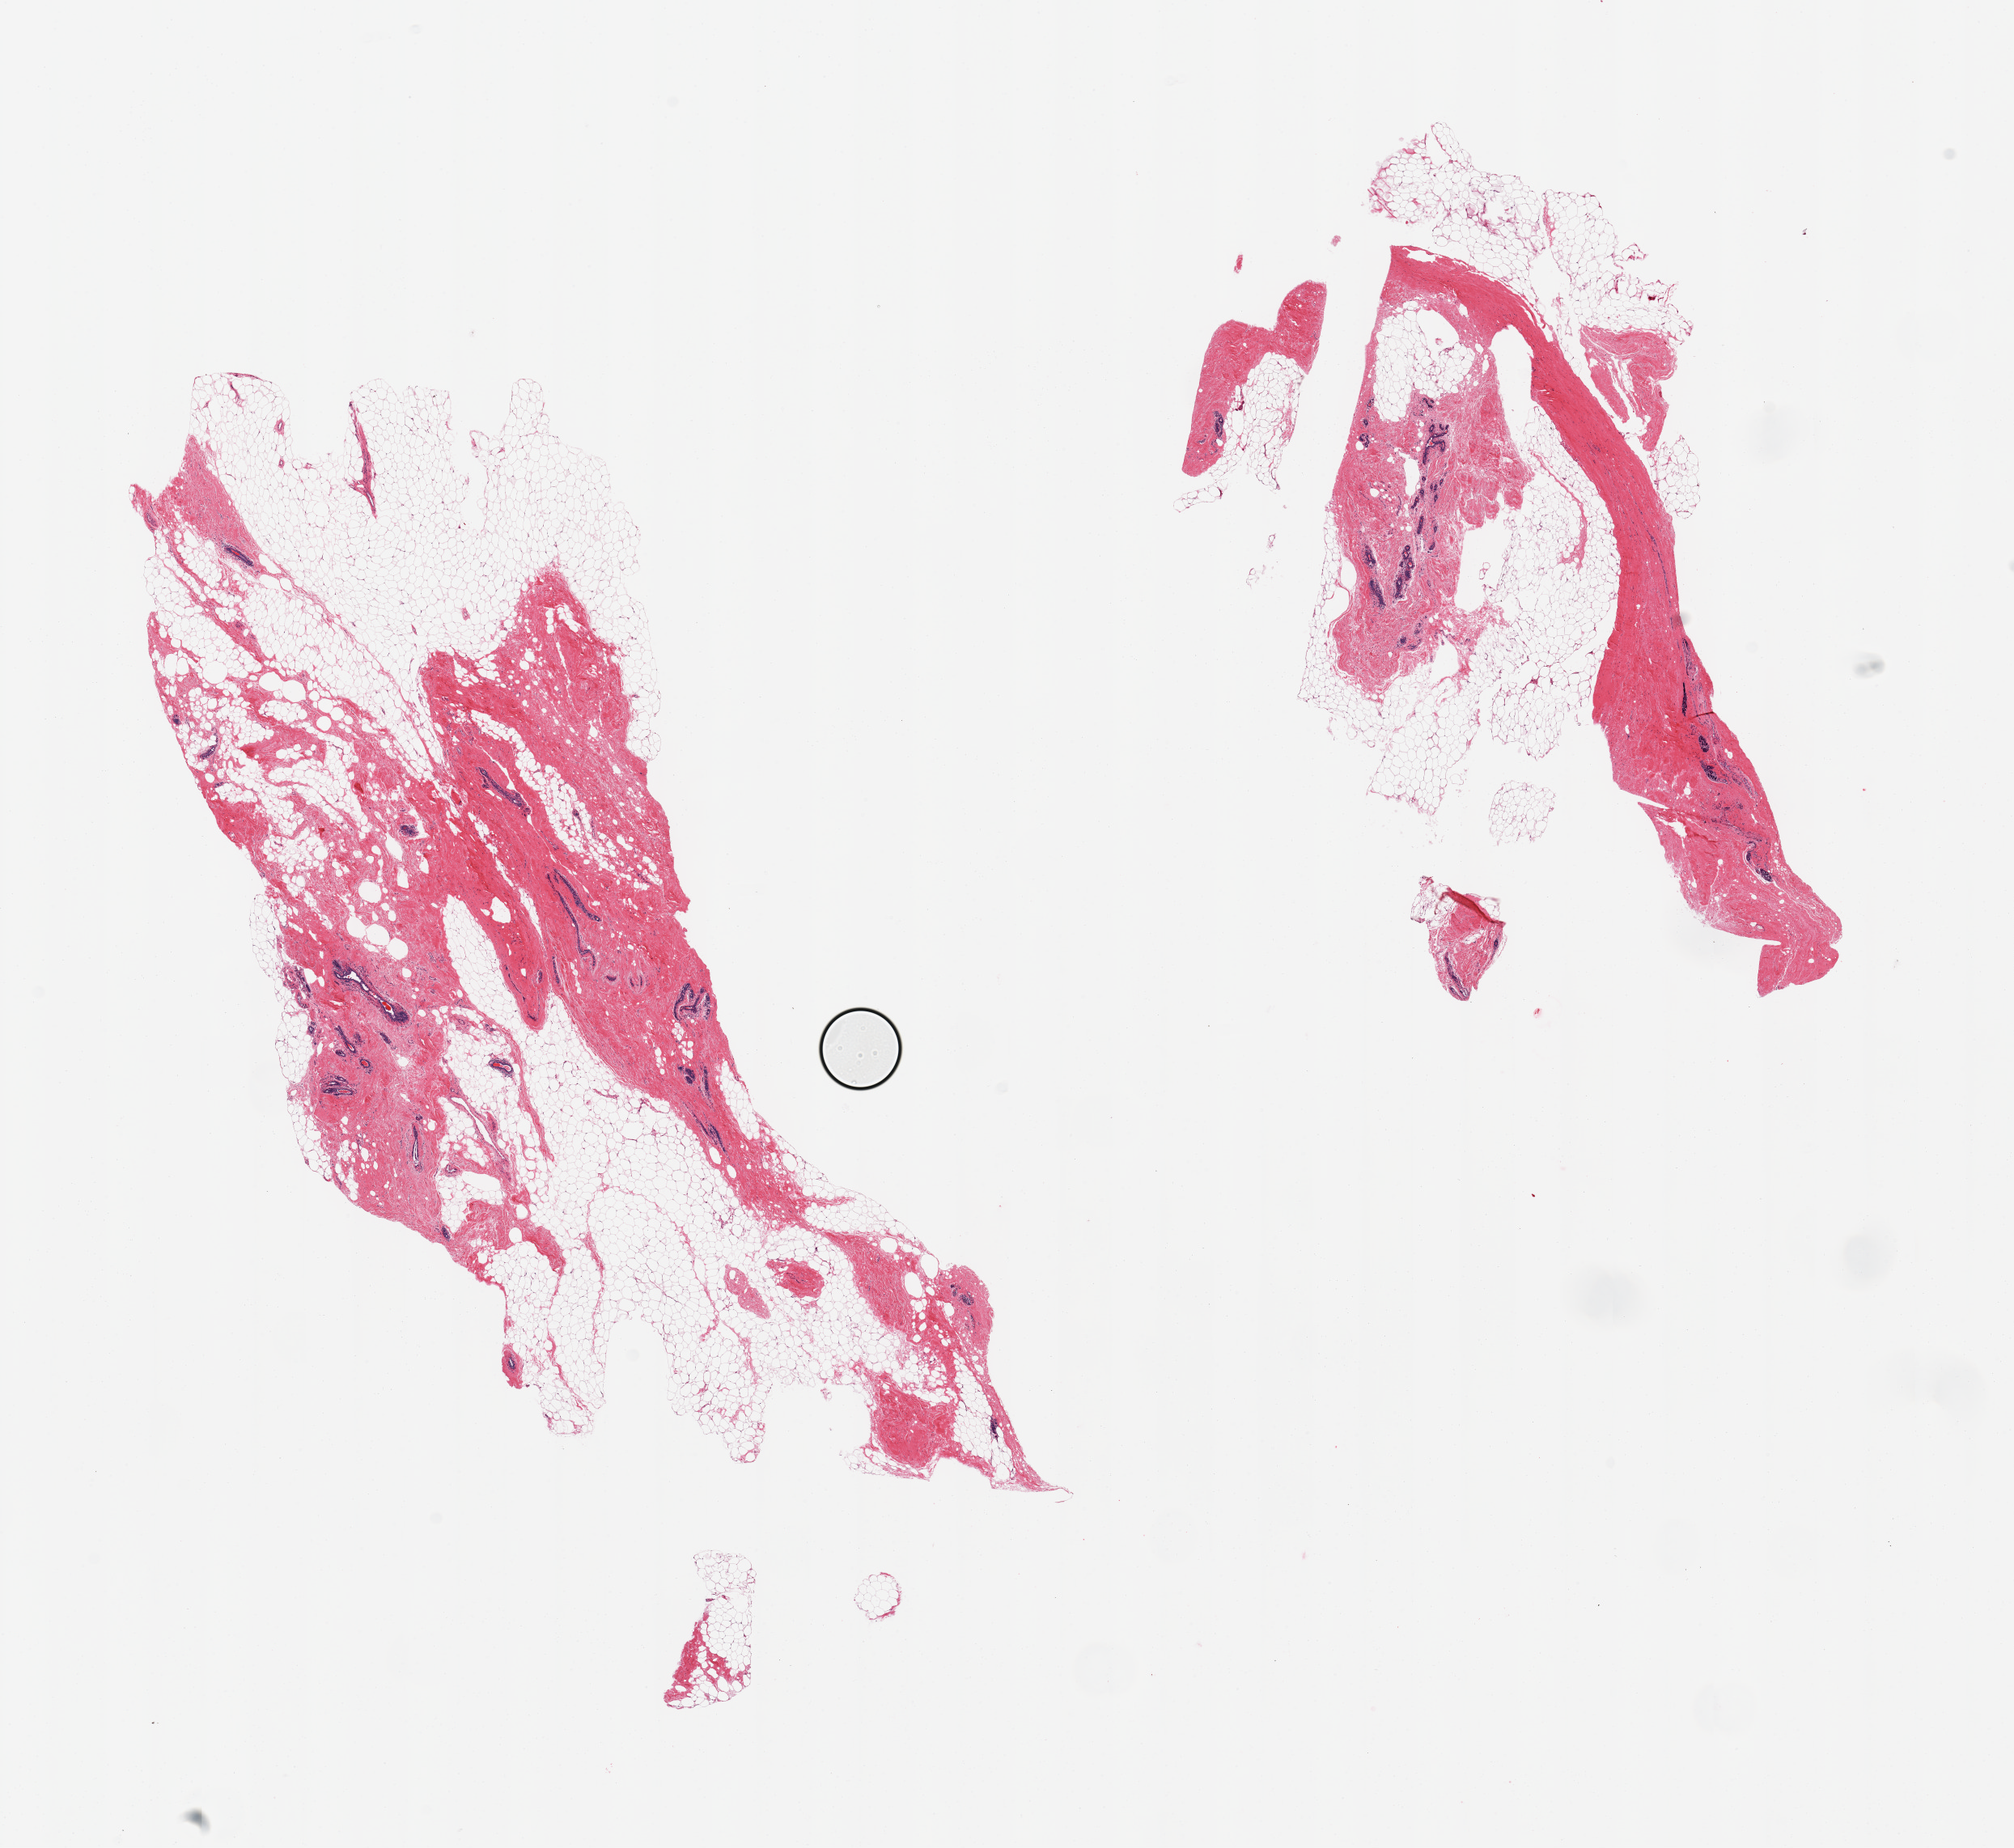
Whole-slide image, H&E stain — a low-resolution overview of the entire scanned area, about 19.7 x 18.1 mm (slide scanned at 20x); PAXgene-fixed, paraffin-embedded tissue; target tissue: breast; tissue donor sample. Female donor.
Pathologist's review note for this sample: 2 pieces, typical post menopausal regressive/atrophic changes; rep TDLUs.